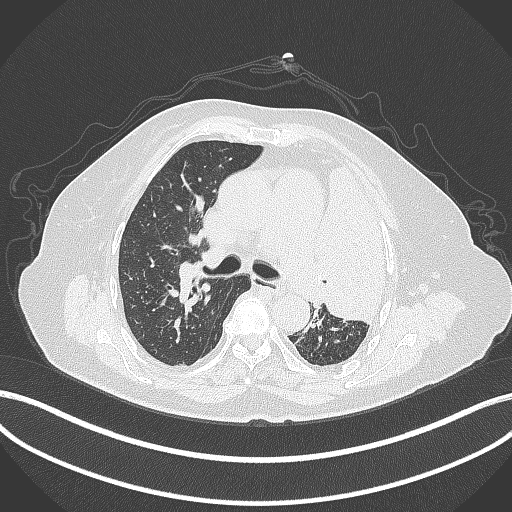
Chest CT, one axial slice. Slice 245 of 399 in the series (ordered by position). Lung window (W 1500 / L -600 HU). 1 mm slice thickness. 512 × 512 image matrix, field of view 400 × 400 mm. Female patient, age 75 years. From the clinical record (not read from this slice): clinical TNM (as recorded): T3 N3 M1.
Outlined on this slice (rectangle marked by the reading radiologist):
- lung tumour (recorded histology: adenocarcinoma): bounding box (x1, y1, x2, y2) in pixels: (315, 156, 393, 322)